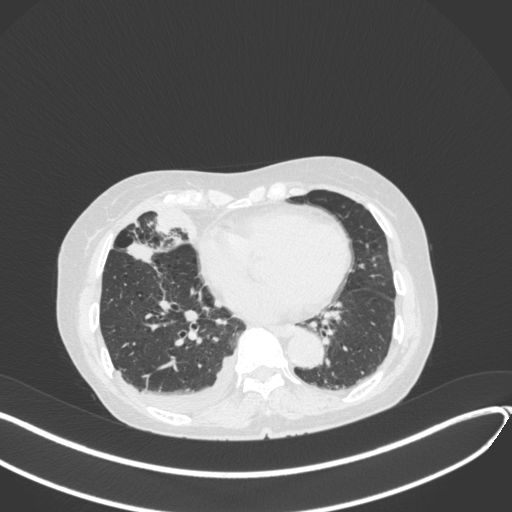
Chest CT, one axial slice; position 148 of 418 along the scan axis; reconstruction kernel B31f; 120 kVp; lung window (W 1500 / L -600 HU); 1 mm slice thickness; 512 × 512 image matrix, field of view 400 × 400 mm. Female patient, age 75 years. From the clinical record (not read from this slice): clinical TNM (as recorded): T2a N3 M0.
Outlined on this slice (rectangle marked by the reading radiologist):
- lung tumour (recorded histology: adenocarcinoma): bounding box (x1, y1, x2, y2) in pixels: (126, 236, 159, 267)